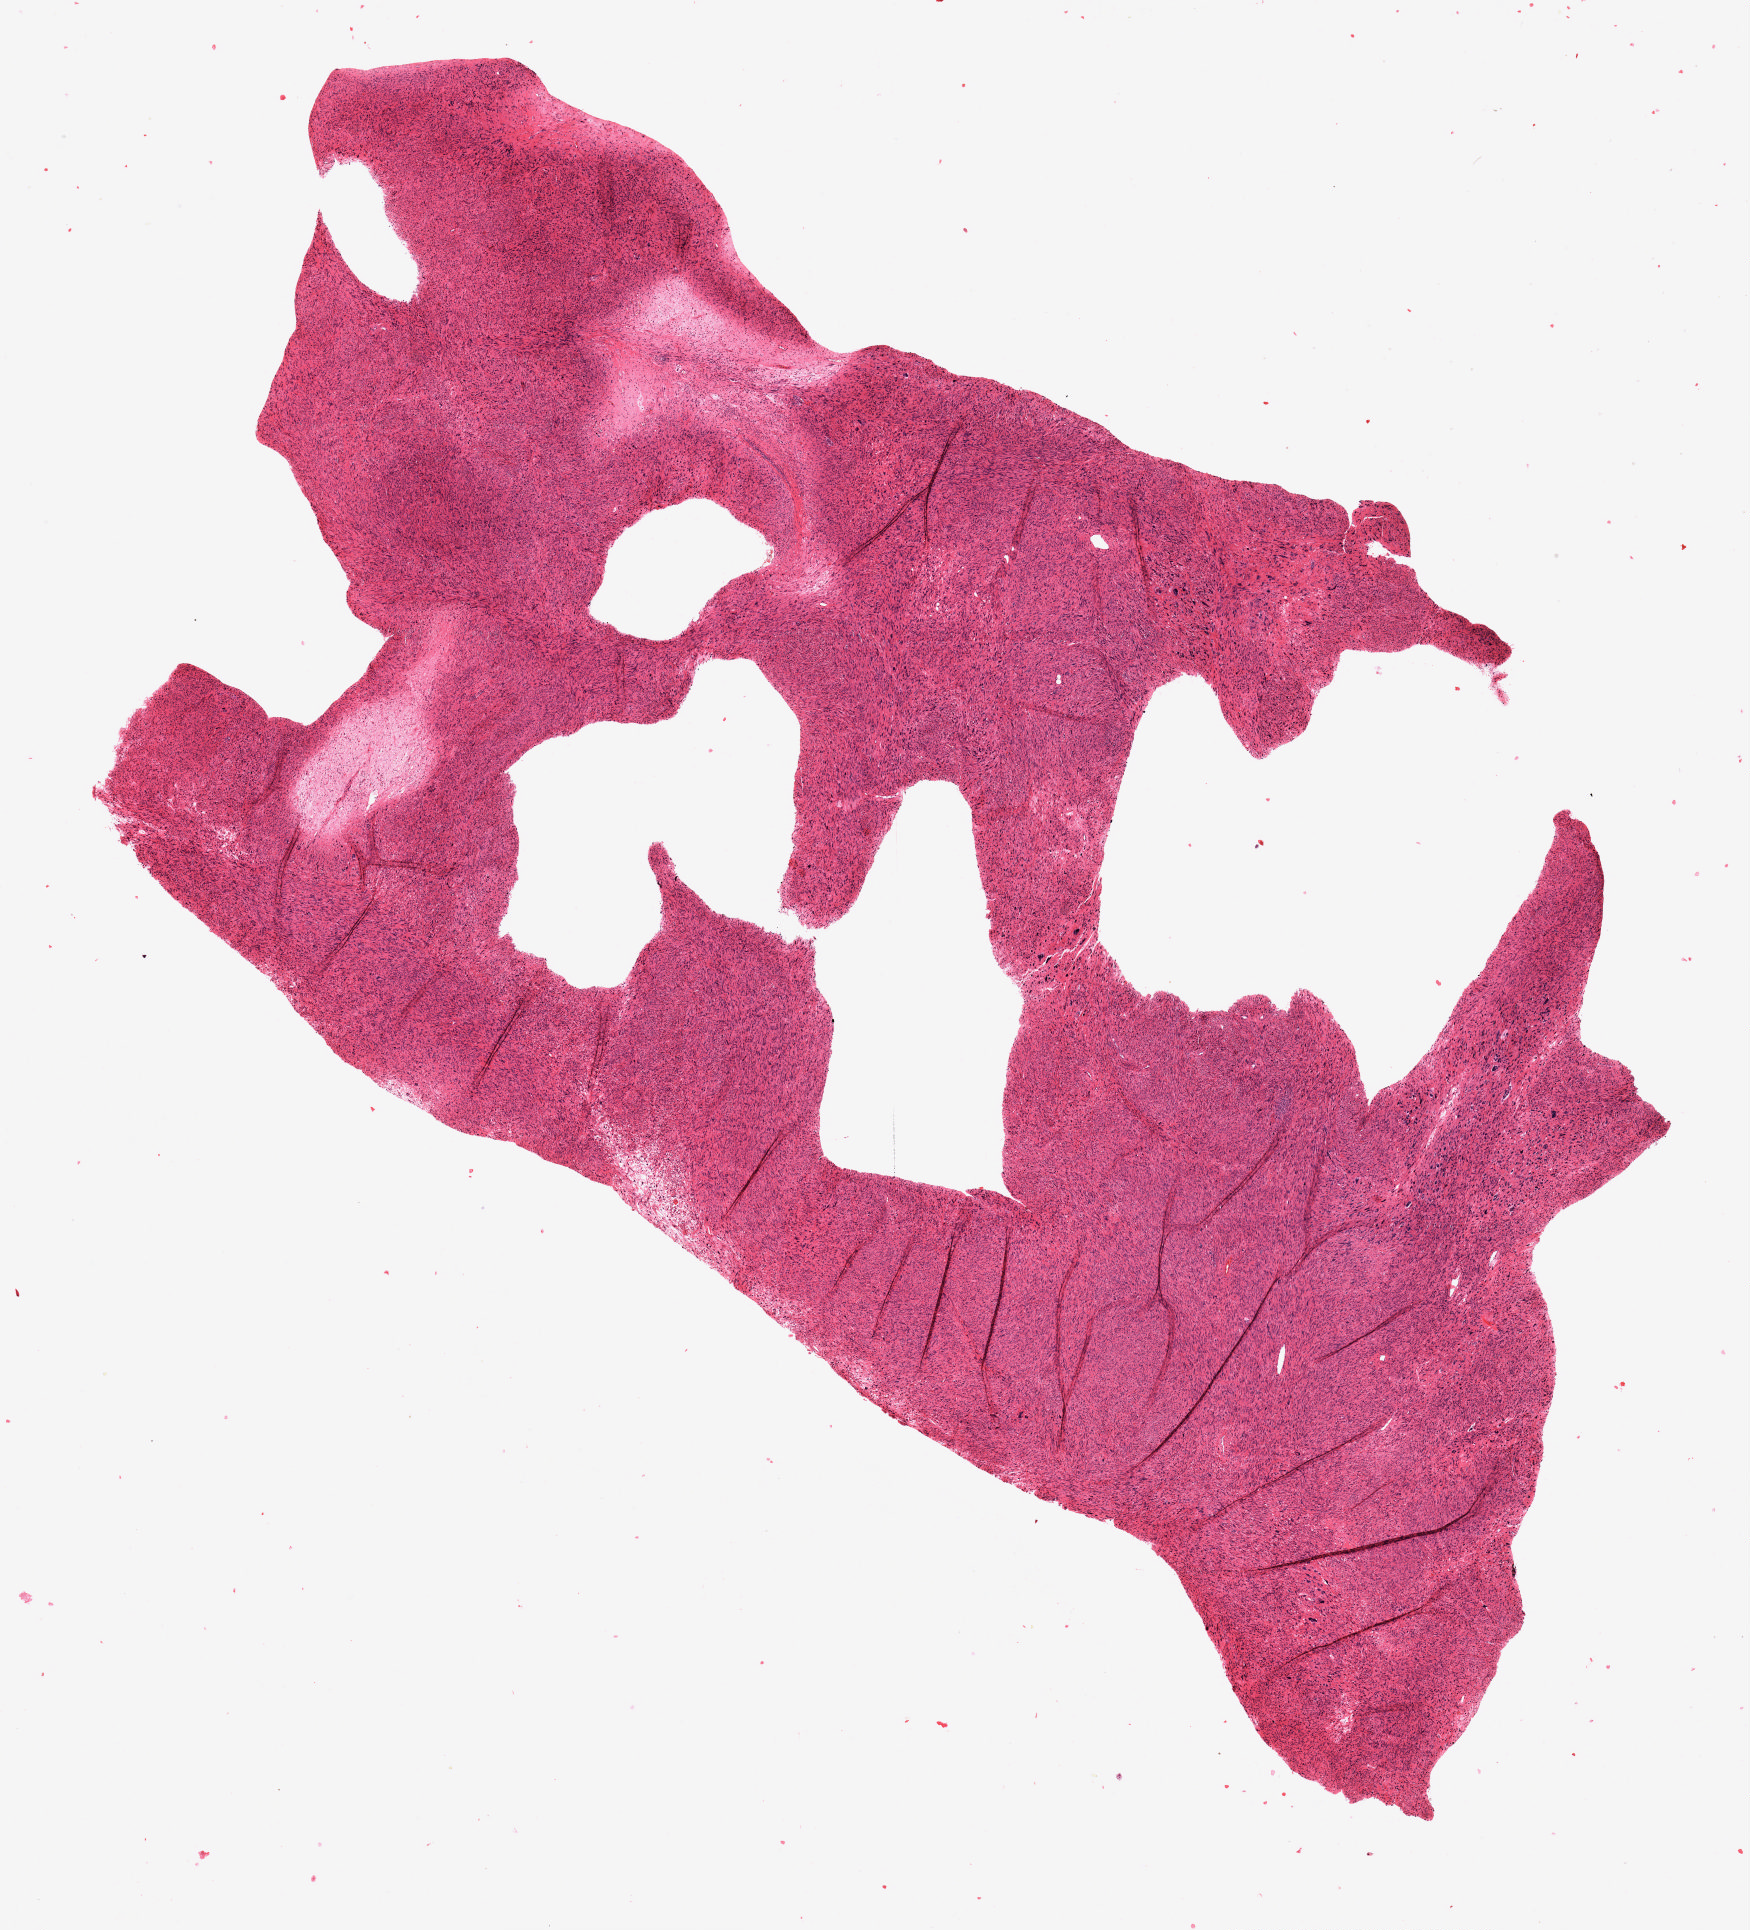
Whole-slide histology image, H&E-stained — shown as a low-resolution overview of the whole scanned area (about 14.0 x 15.4 mm). Formalin-fixed paraffin-embedded (FFPE) diagnostic section. Primary tumour sample from the connective, subcutaneous and other soft tissues. Patient sex: male.
Histologic diagnosis: Undifferentiated sarcoma (connective, subcutaneous and other soft tissues of lower limb and hip).